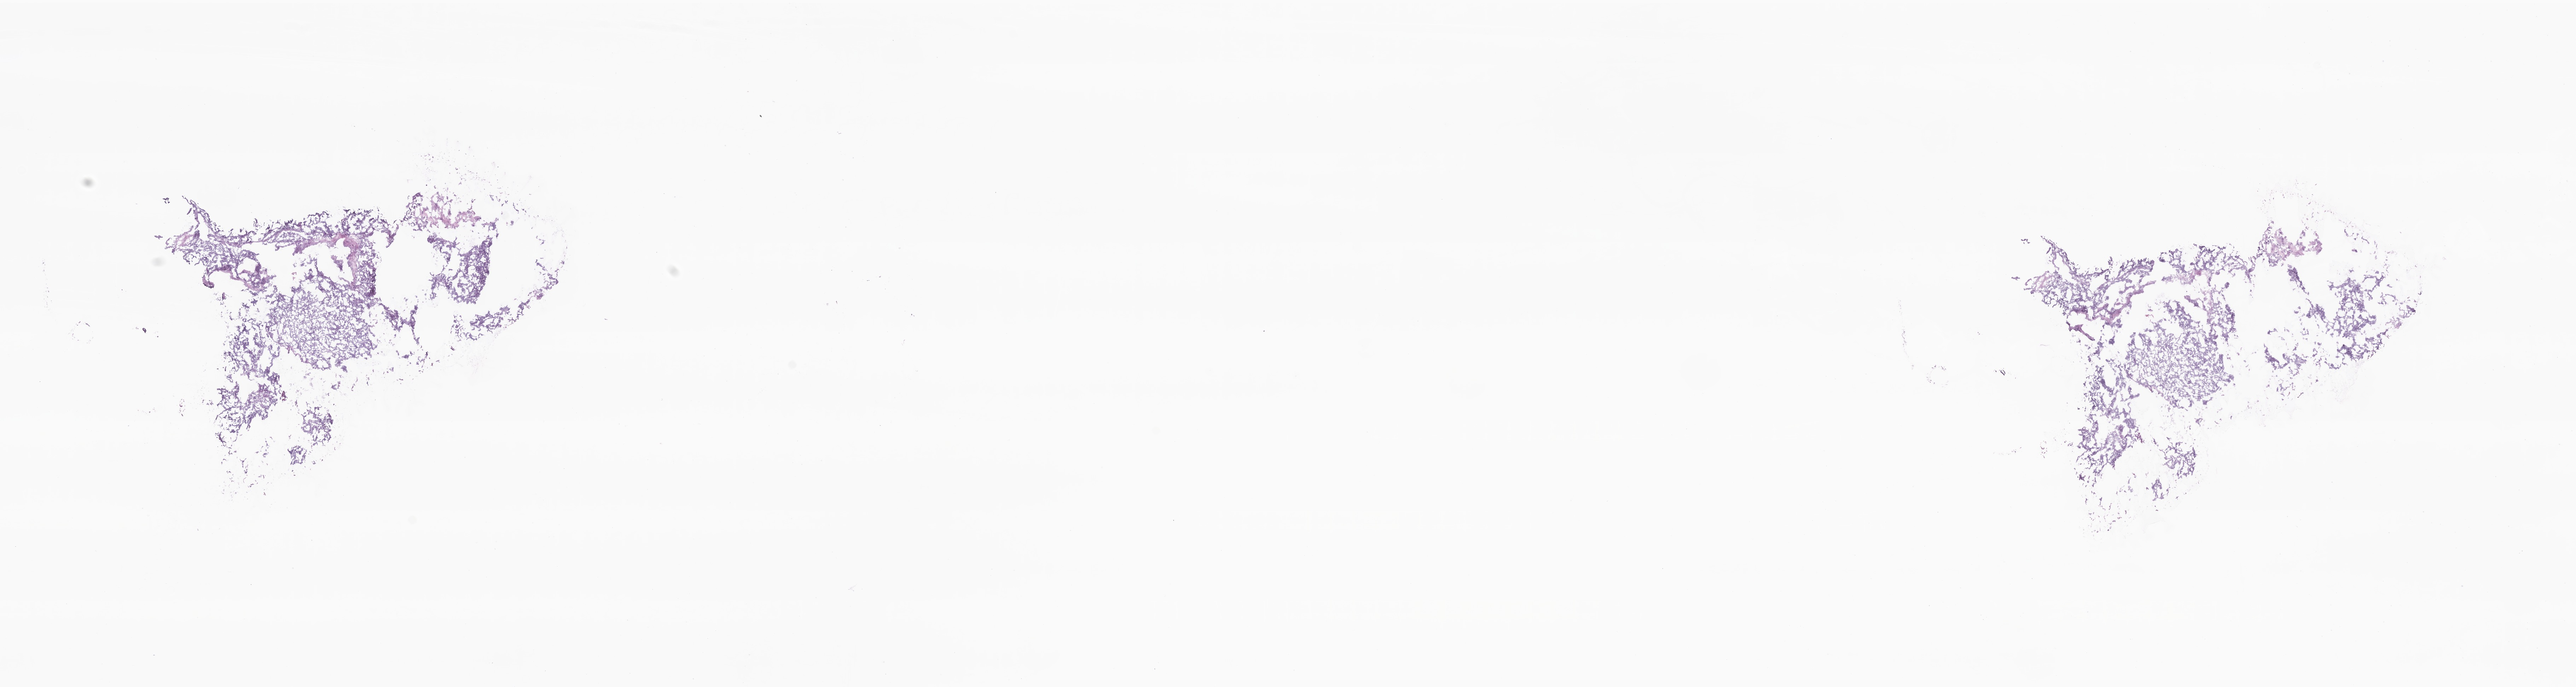
Haematoxylin and eosin whole-slide image — low-resolution overview of the scanned area, about 30.7 x 8.2 mm, cryosection, primary tumor, site: kidney. Male, age 50 years at initial diagnosis. Tumor grade: G3 (poorly differentiated). Pathologist review of this section (percent, as recorded): tumor cells 87%, tumor nuclei 93%, stromal cells 6%, necrosis 0%, normal cells 7%. Infiltration values recorded for this section: lymphocyte infiltration 0%, monocyte infiltration 0%, neutrophil infiltration 0%.
AJCC pathologic stage: Stage III. Section: bottom of the tissue portion. Histologic diagnosis: Clear cell adenocarcinoma, NOS.